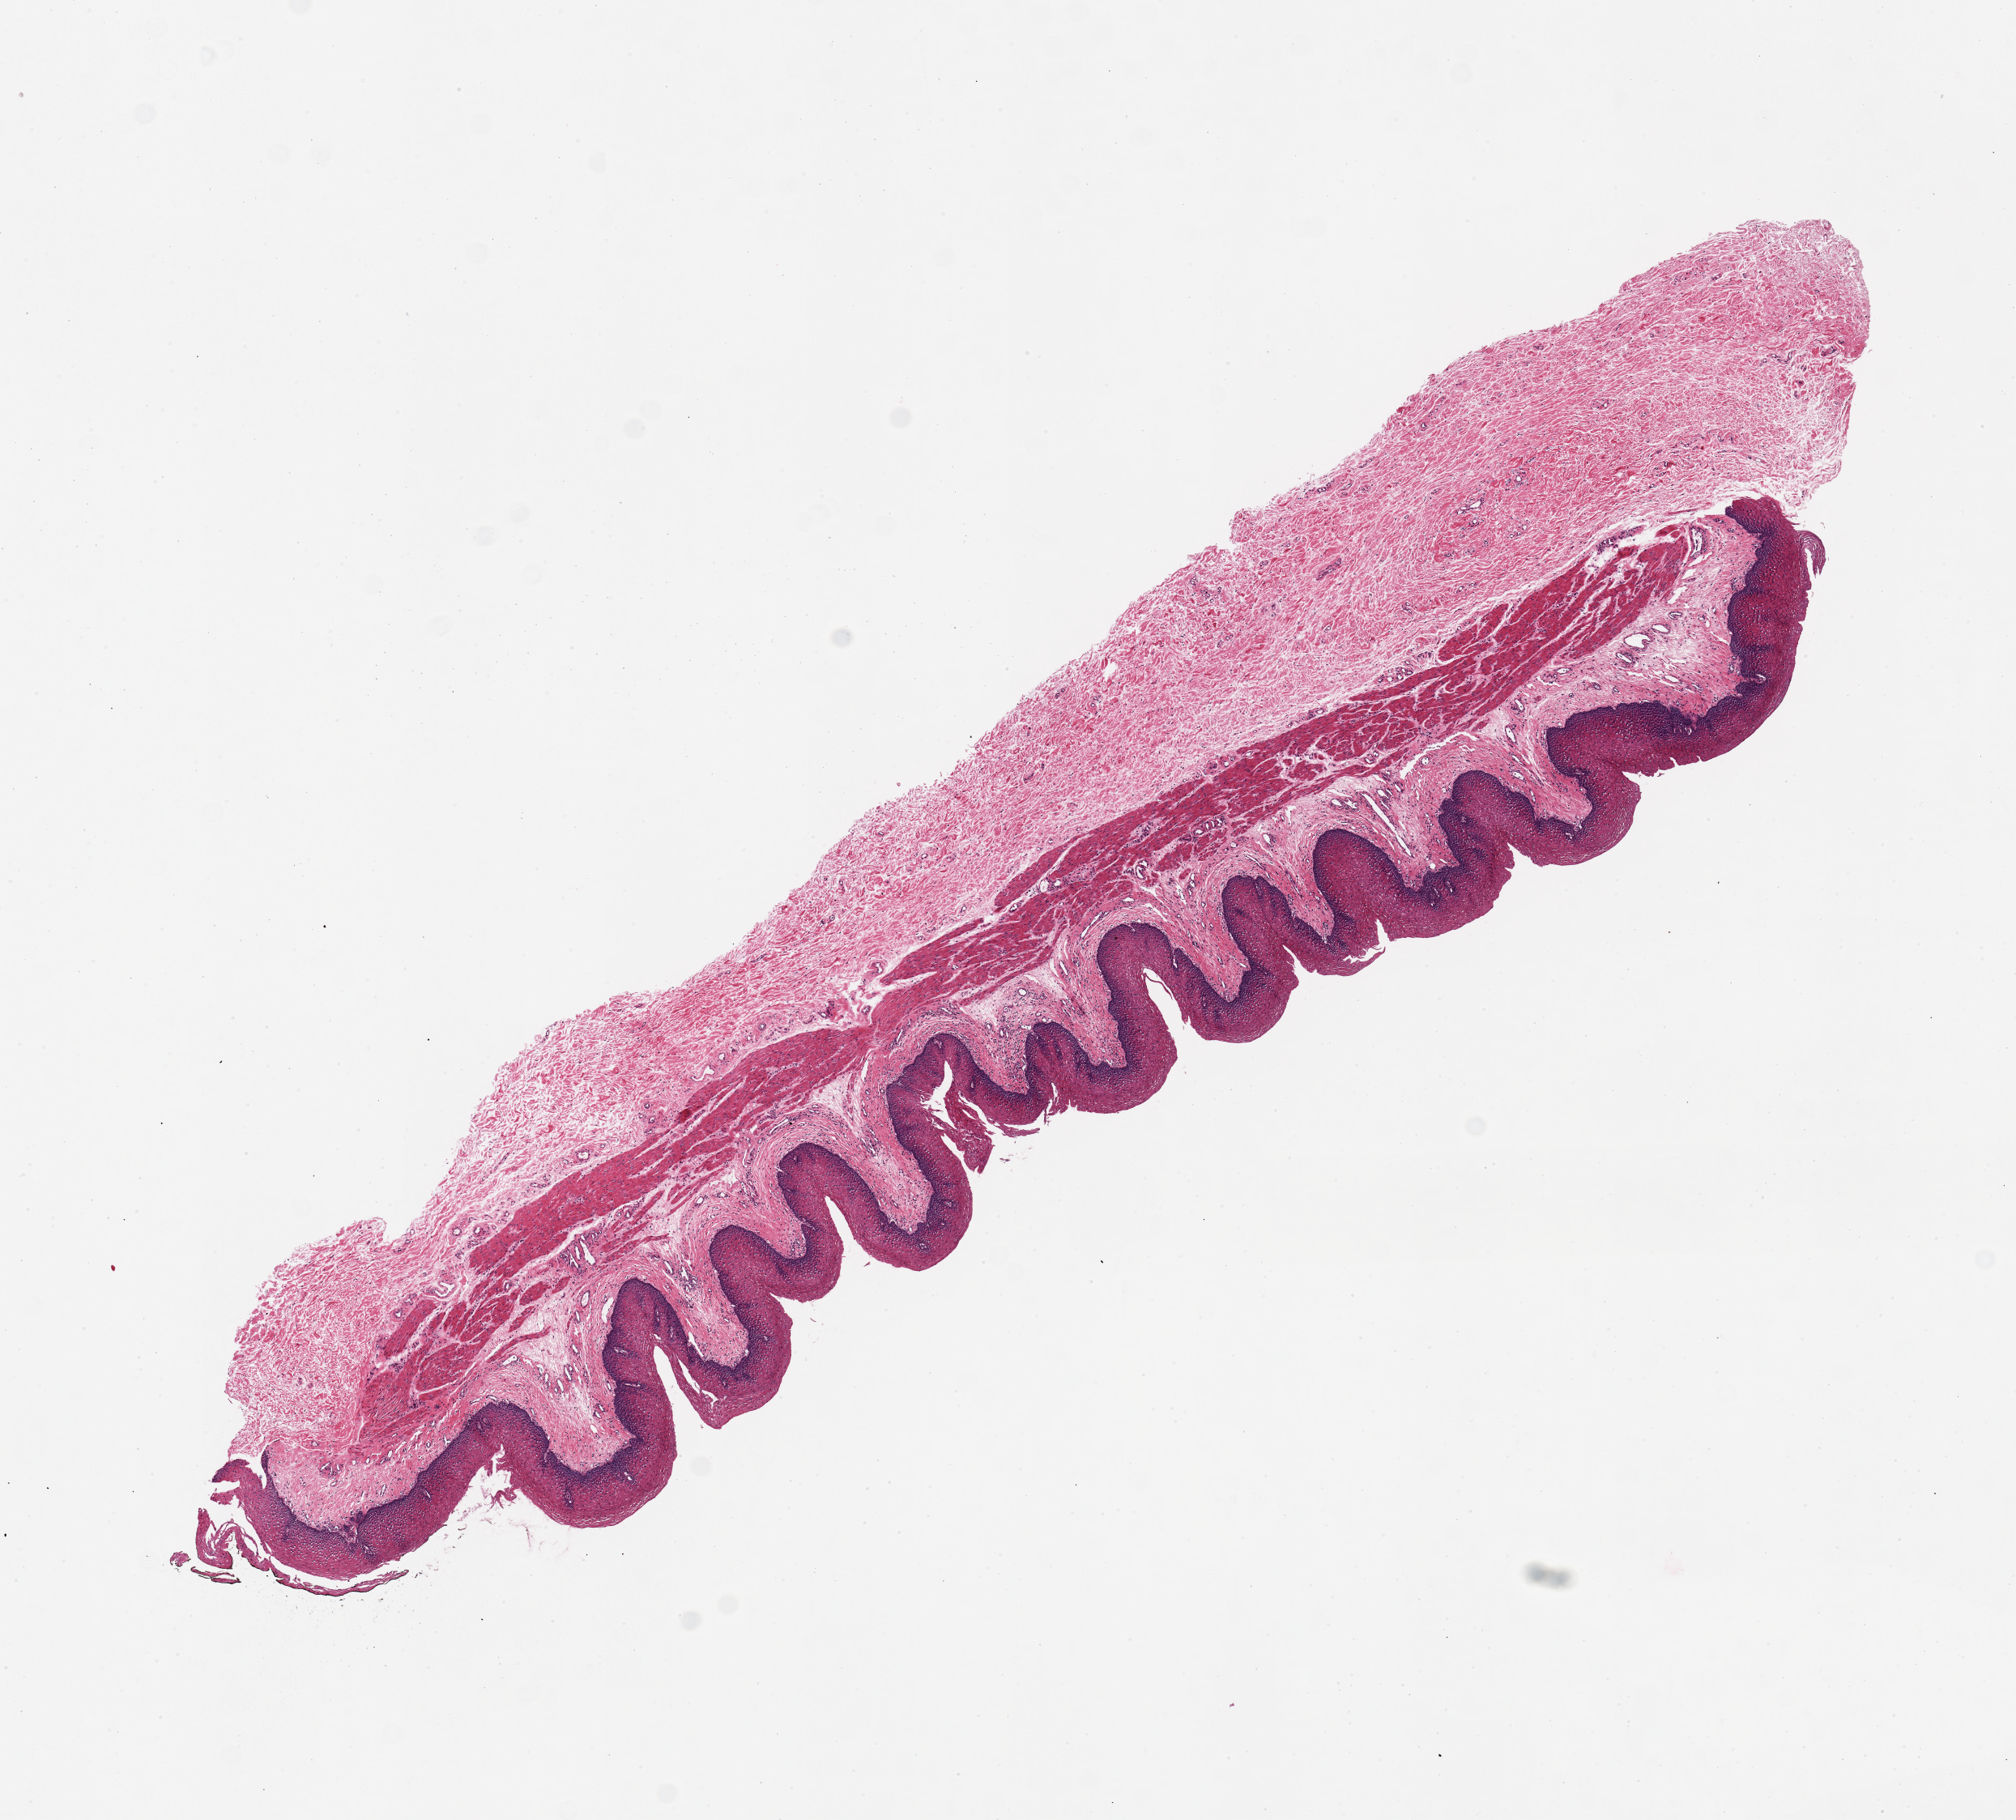
H&E whole-slide image, whole scanned area (about 9.8 x 8.9 mm, from a 20x scan) shown as a low-resolution overview, PAXgene-fixed paraffin-embedded (PFPE) section, section of esophageal mucous membrane (target tissue), tissue donor sample. Male donor.
- reviewer comment on this tissue sample: 1 piece, 10x2.5 mm. Focal surface desquamation